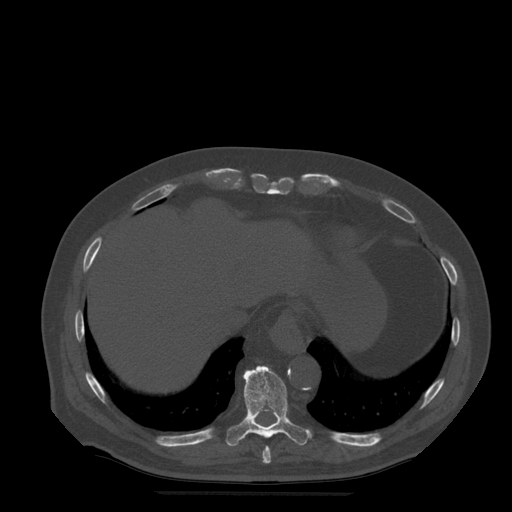
CT including the spine, one axial slice; slice 270 of 522 in the series (ordered by position); bone window (W 1800 / L 400 HU); 512 × 512 image matrix, field of view 420 × 420 mm. Patient age 72 years. Case-level facts recorded for this patient, not image findings: primary cancer: prostate.
Structures marked on this image (semi-automatically segmented with operator editing):
- T10 vertebra: bounding box <226,366,312,446> (left, top, right, bottom; pixels)
- T9 vertebra: <263,446,272,464>